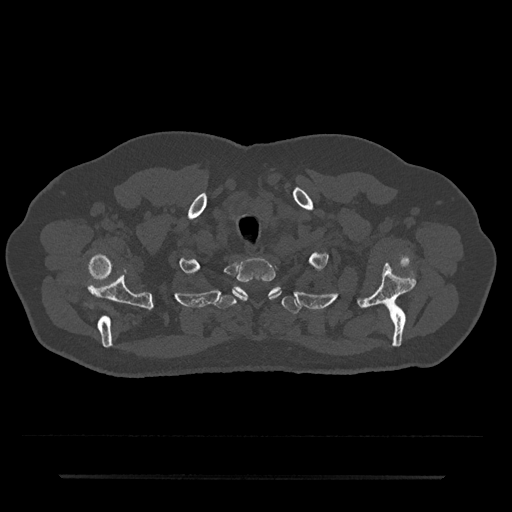
CT including the spine, one axial slice; slice 625 of 797 in the series (ordered by position); bone window (W 1800 / L 400 HU); 0.5 mm slice thickness; 512 × 512 image matrix, field of view 437 × 437 mm. Male patient, age 69 years. Case-level facts recorded for this patient, not image findings: primary cancer: prostate.
Outlined on this slice (semi-automatically segmented with operator editing):
- T1 vertebra: bounding box (x1, y1, x2, y2) in pixels: (233, 258, 281, 300)
- T2 vertebra: (216, 287, 300, 314)